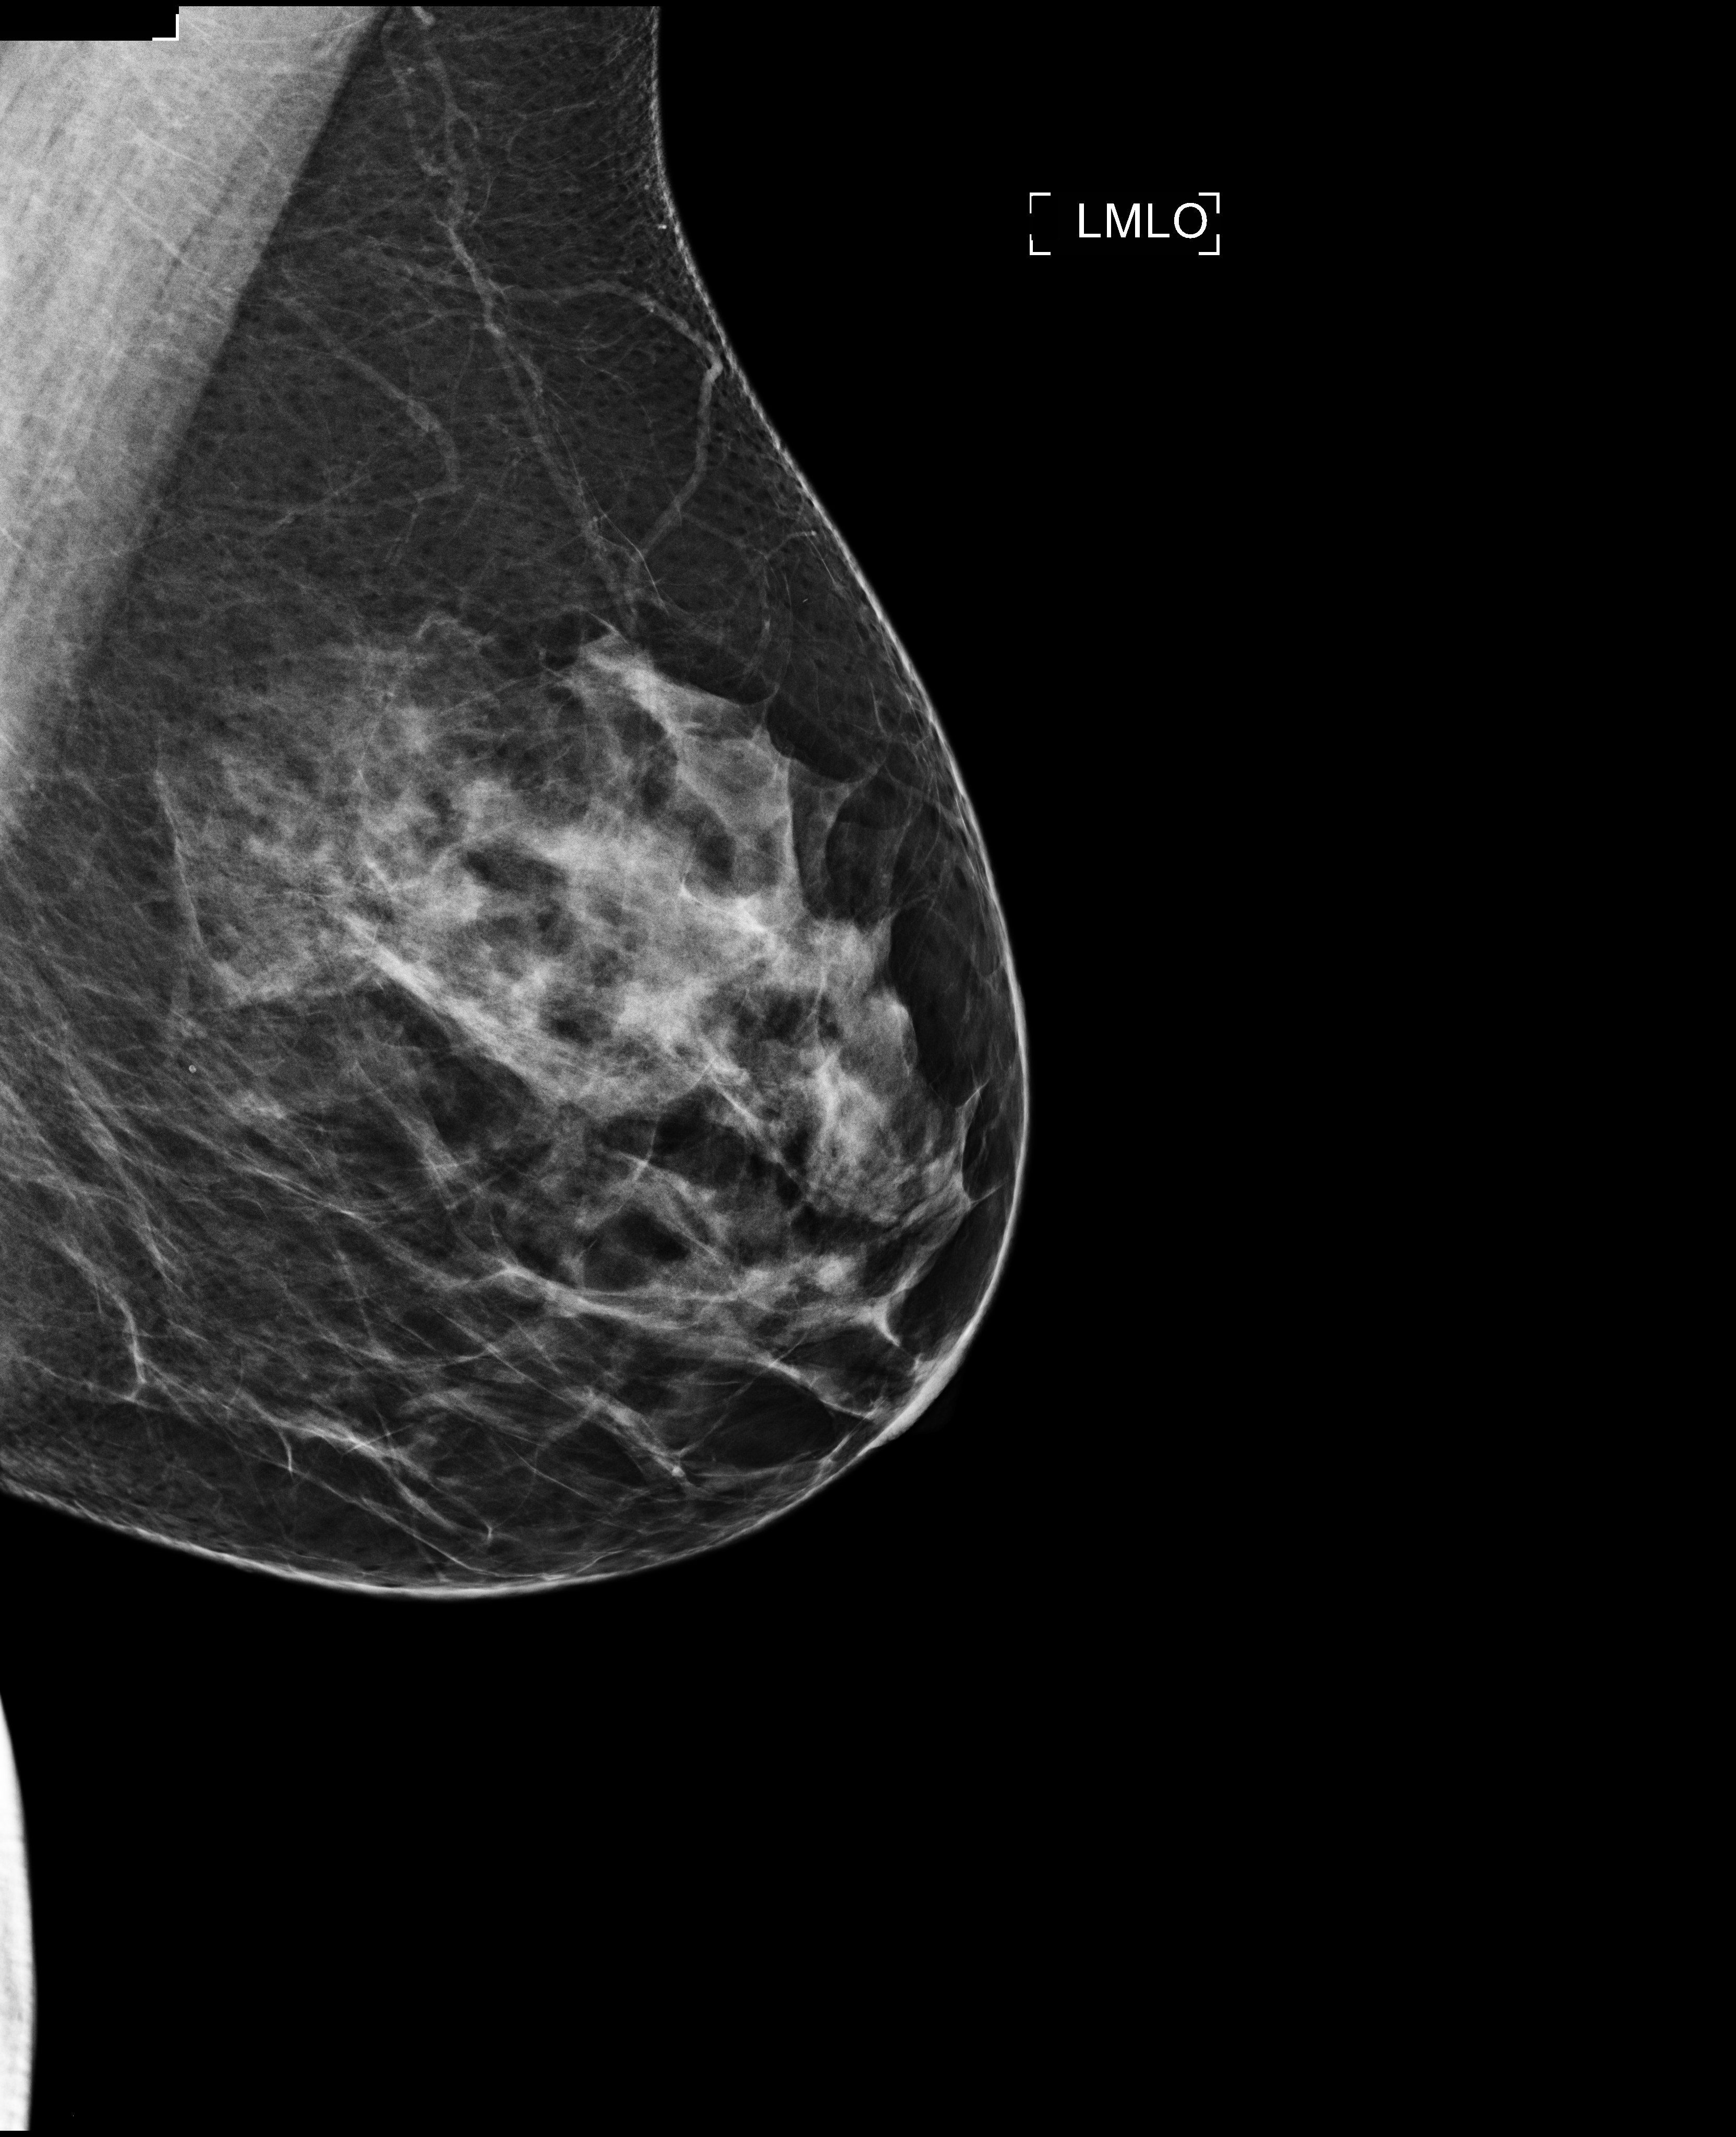
Digital mammogram (FFDM); left breast; mediolateral oblique (MLO) view; screening examination; system: Selenia Dimensions. Female patient, age 45 years.
BI-RADS breast density category at the screening exam (both breasts, scale 1–4): 3. Final BI-RADS assessment for this screening round (tomosynthesis exam, both breasts): category 1. Recall: no recall after this screen.